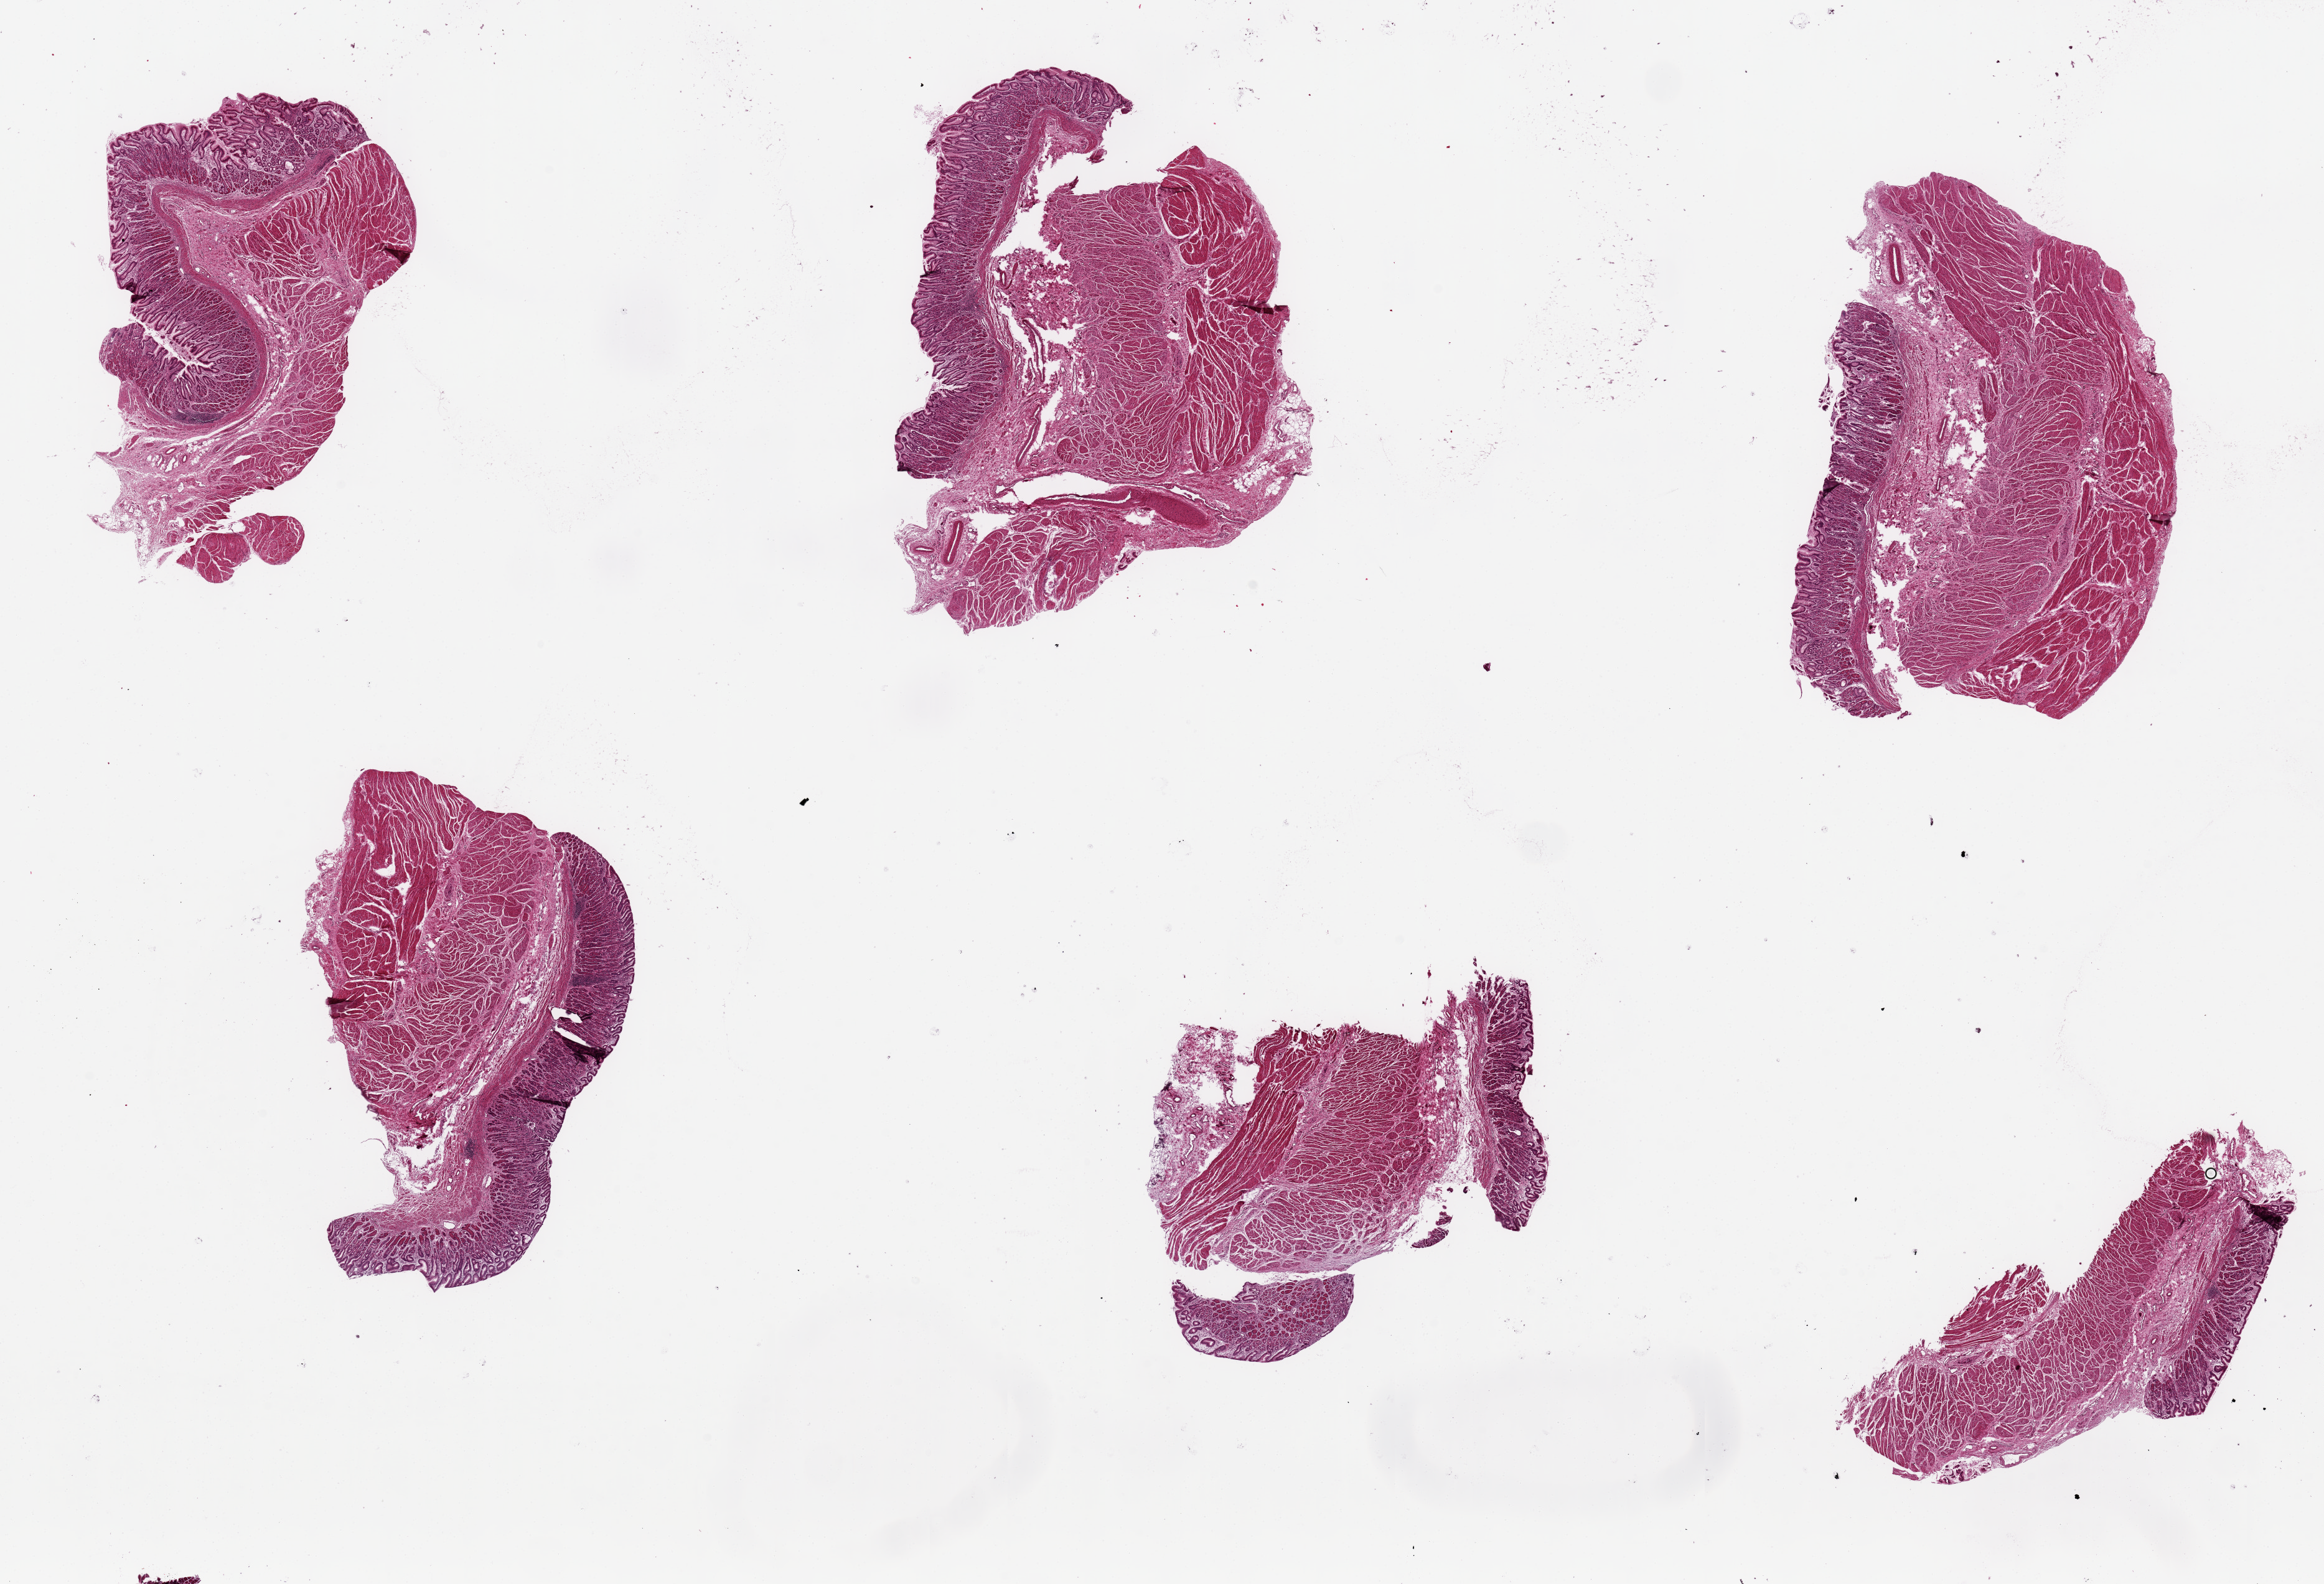
Whole-slide image, haematoxylin and eosin stain — whole scanned area (about 29.5 x 20.1 mm, slide scanned at 20x) shown as a low-resolution overview, PAXgene-fixed, paraffin-embedded tissue, section of gastroesophageal junction (target tissue), tissue donor sample. Donor sex: male.
• reviewer comment on this tissue sample: 6 pieces ~7x4mm, up to 20% adherent gastric cardiac mucosa; Can be retained, focus should be on muscularis only; Sample with caution